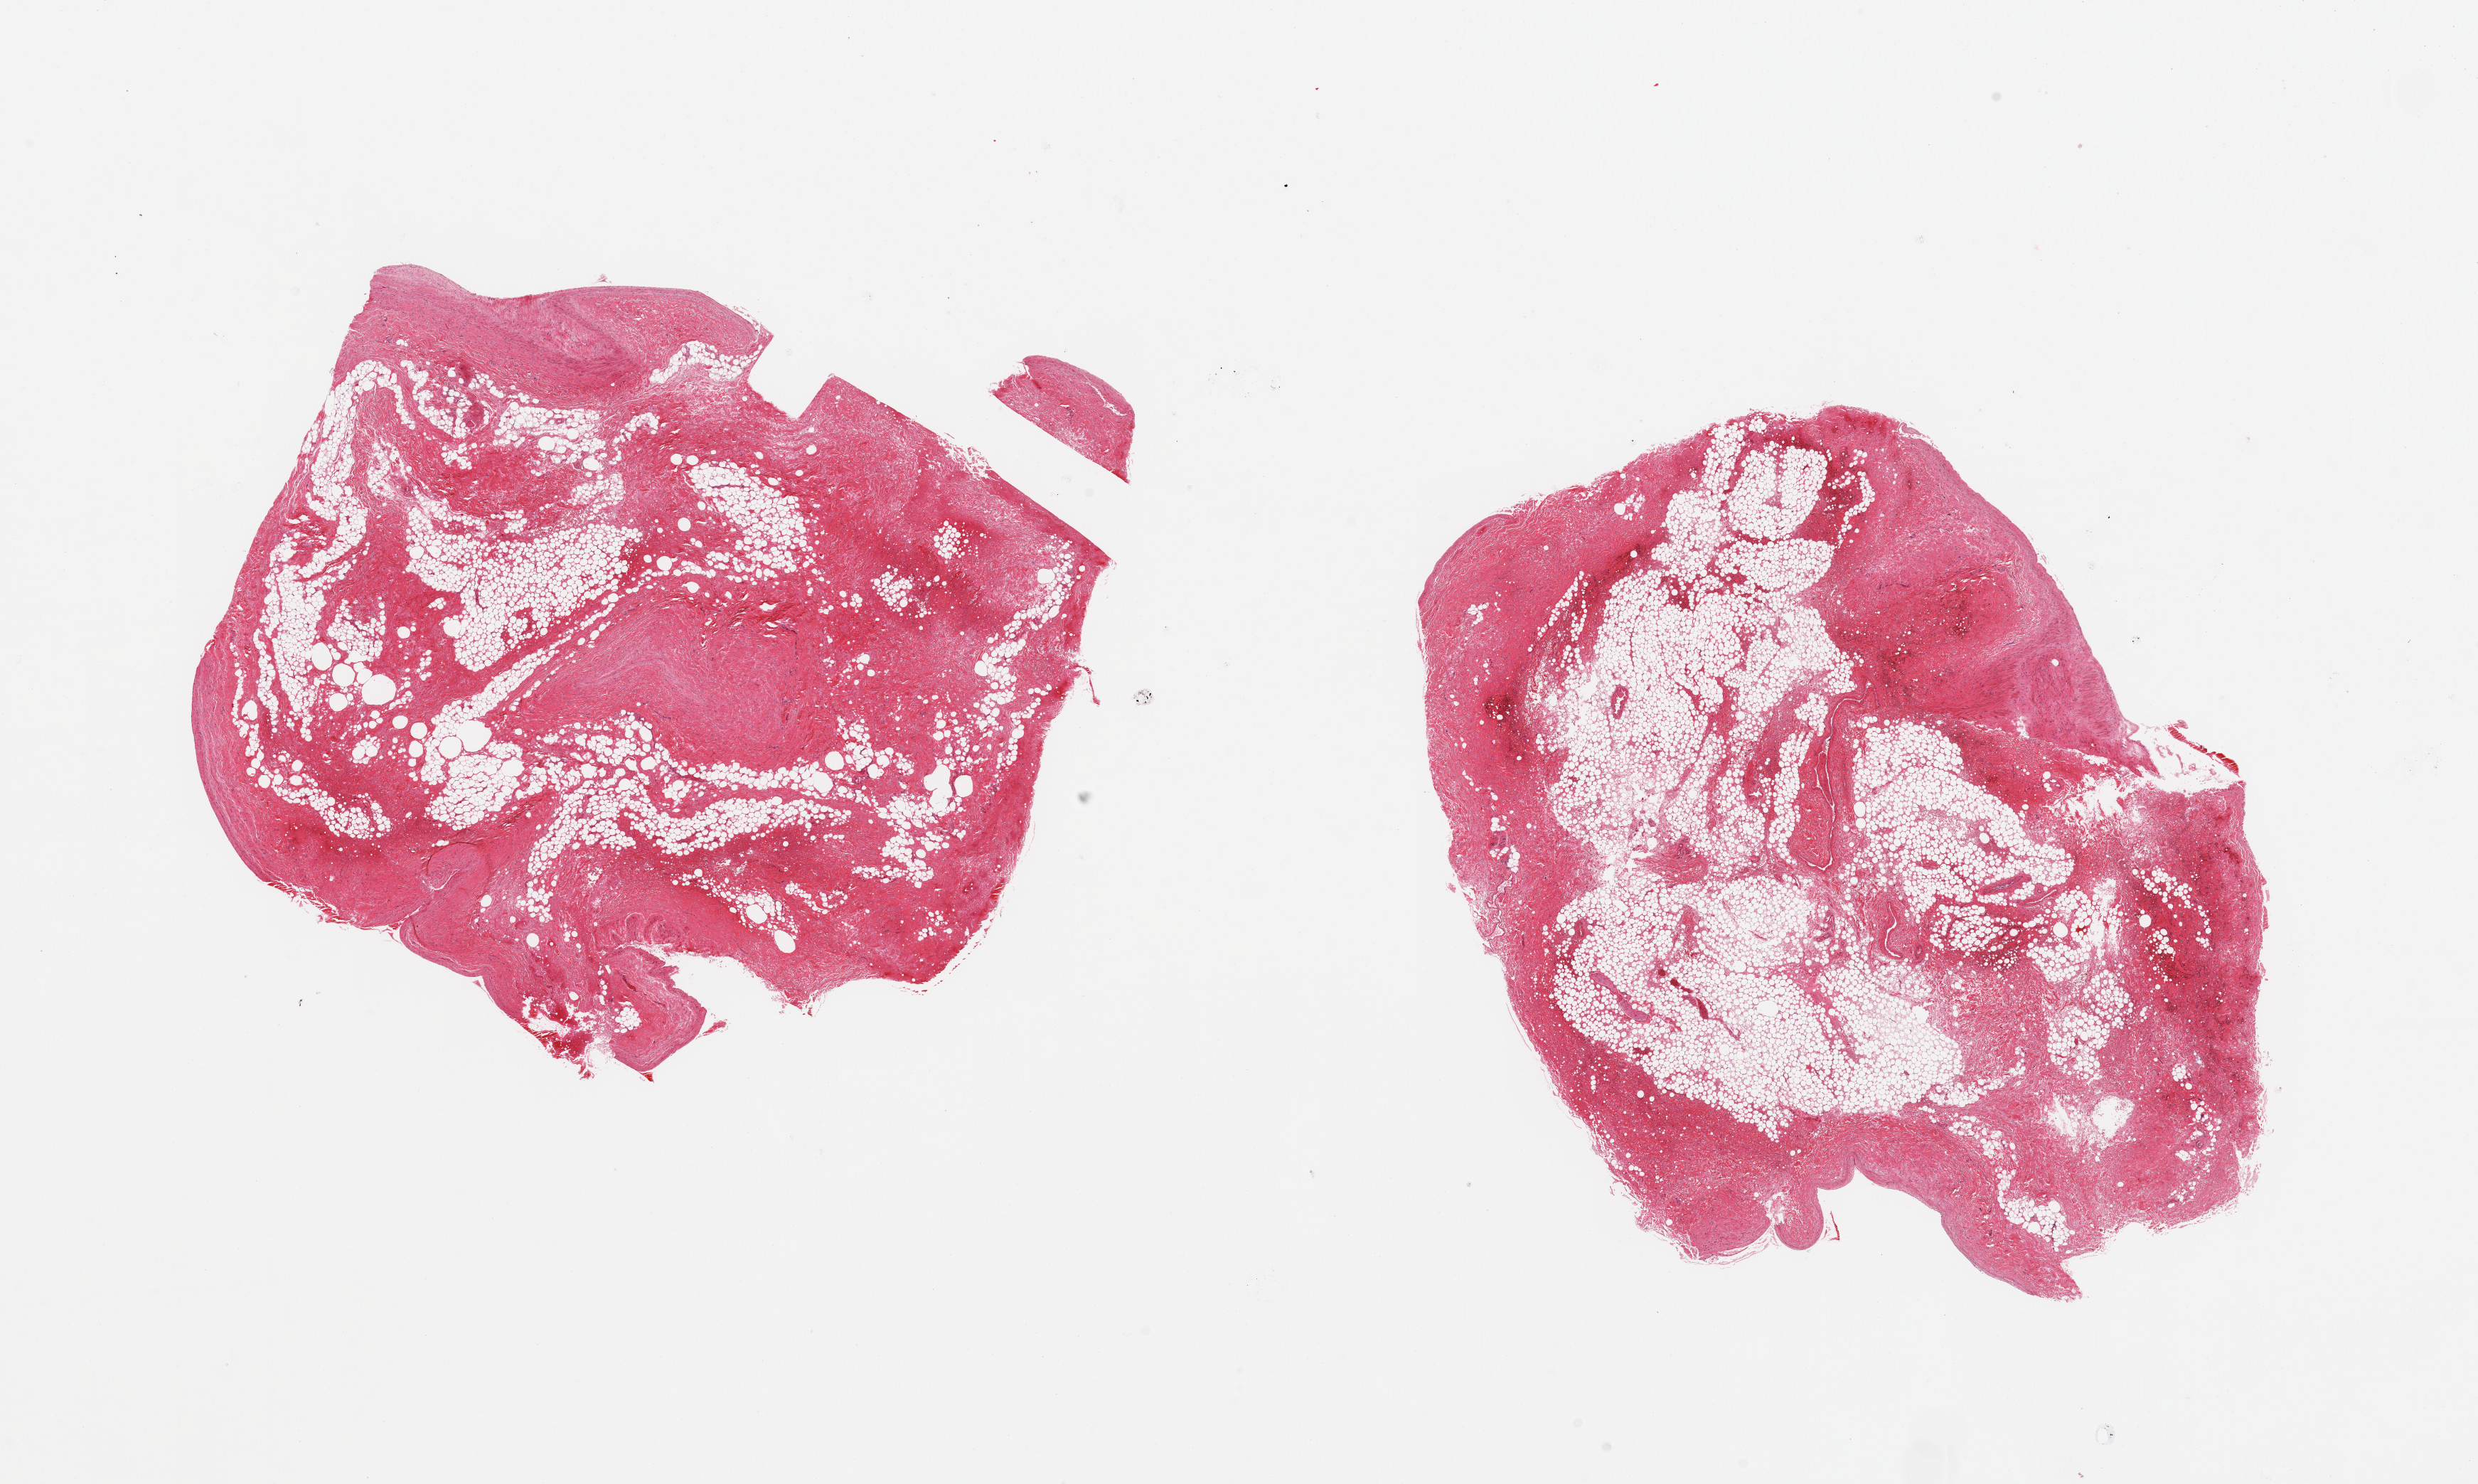
Digitized H&E-stained section, low-resolution overview of the scanned area, about 27.6 x 16.5 mm, PAXgene-fixed paraffin-embedded (PFPE) section, target tissue: auricular appendage, donor tissue sample. Male donor.
• review note (as recorded): 2 pieces; fat and fibrous tissue only